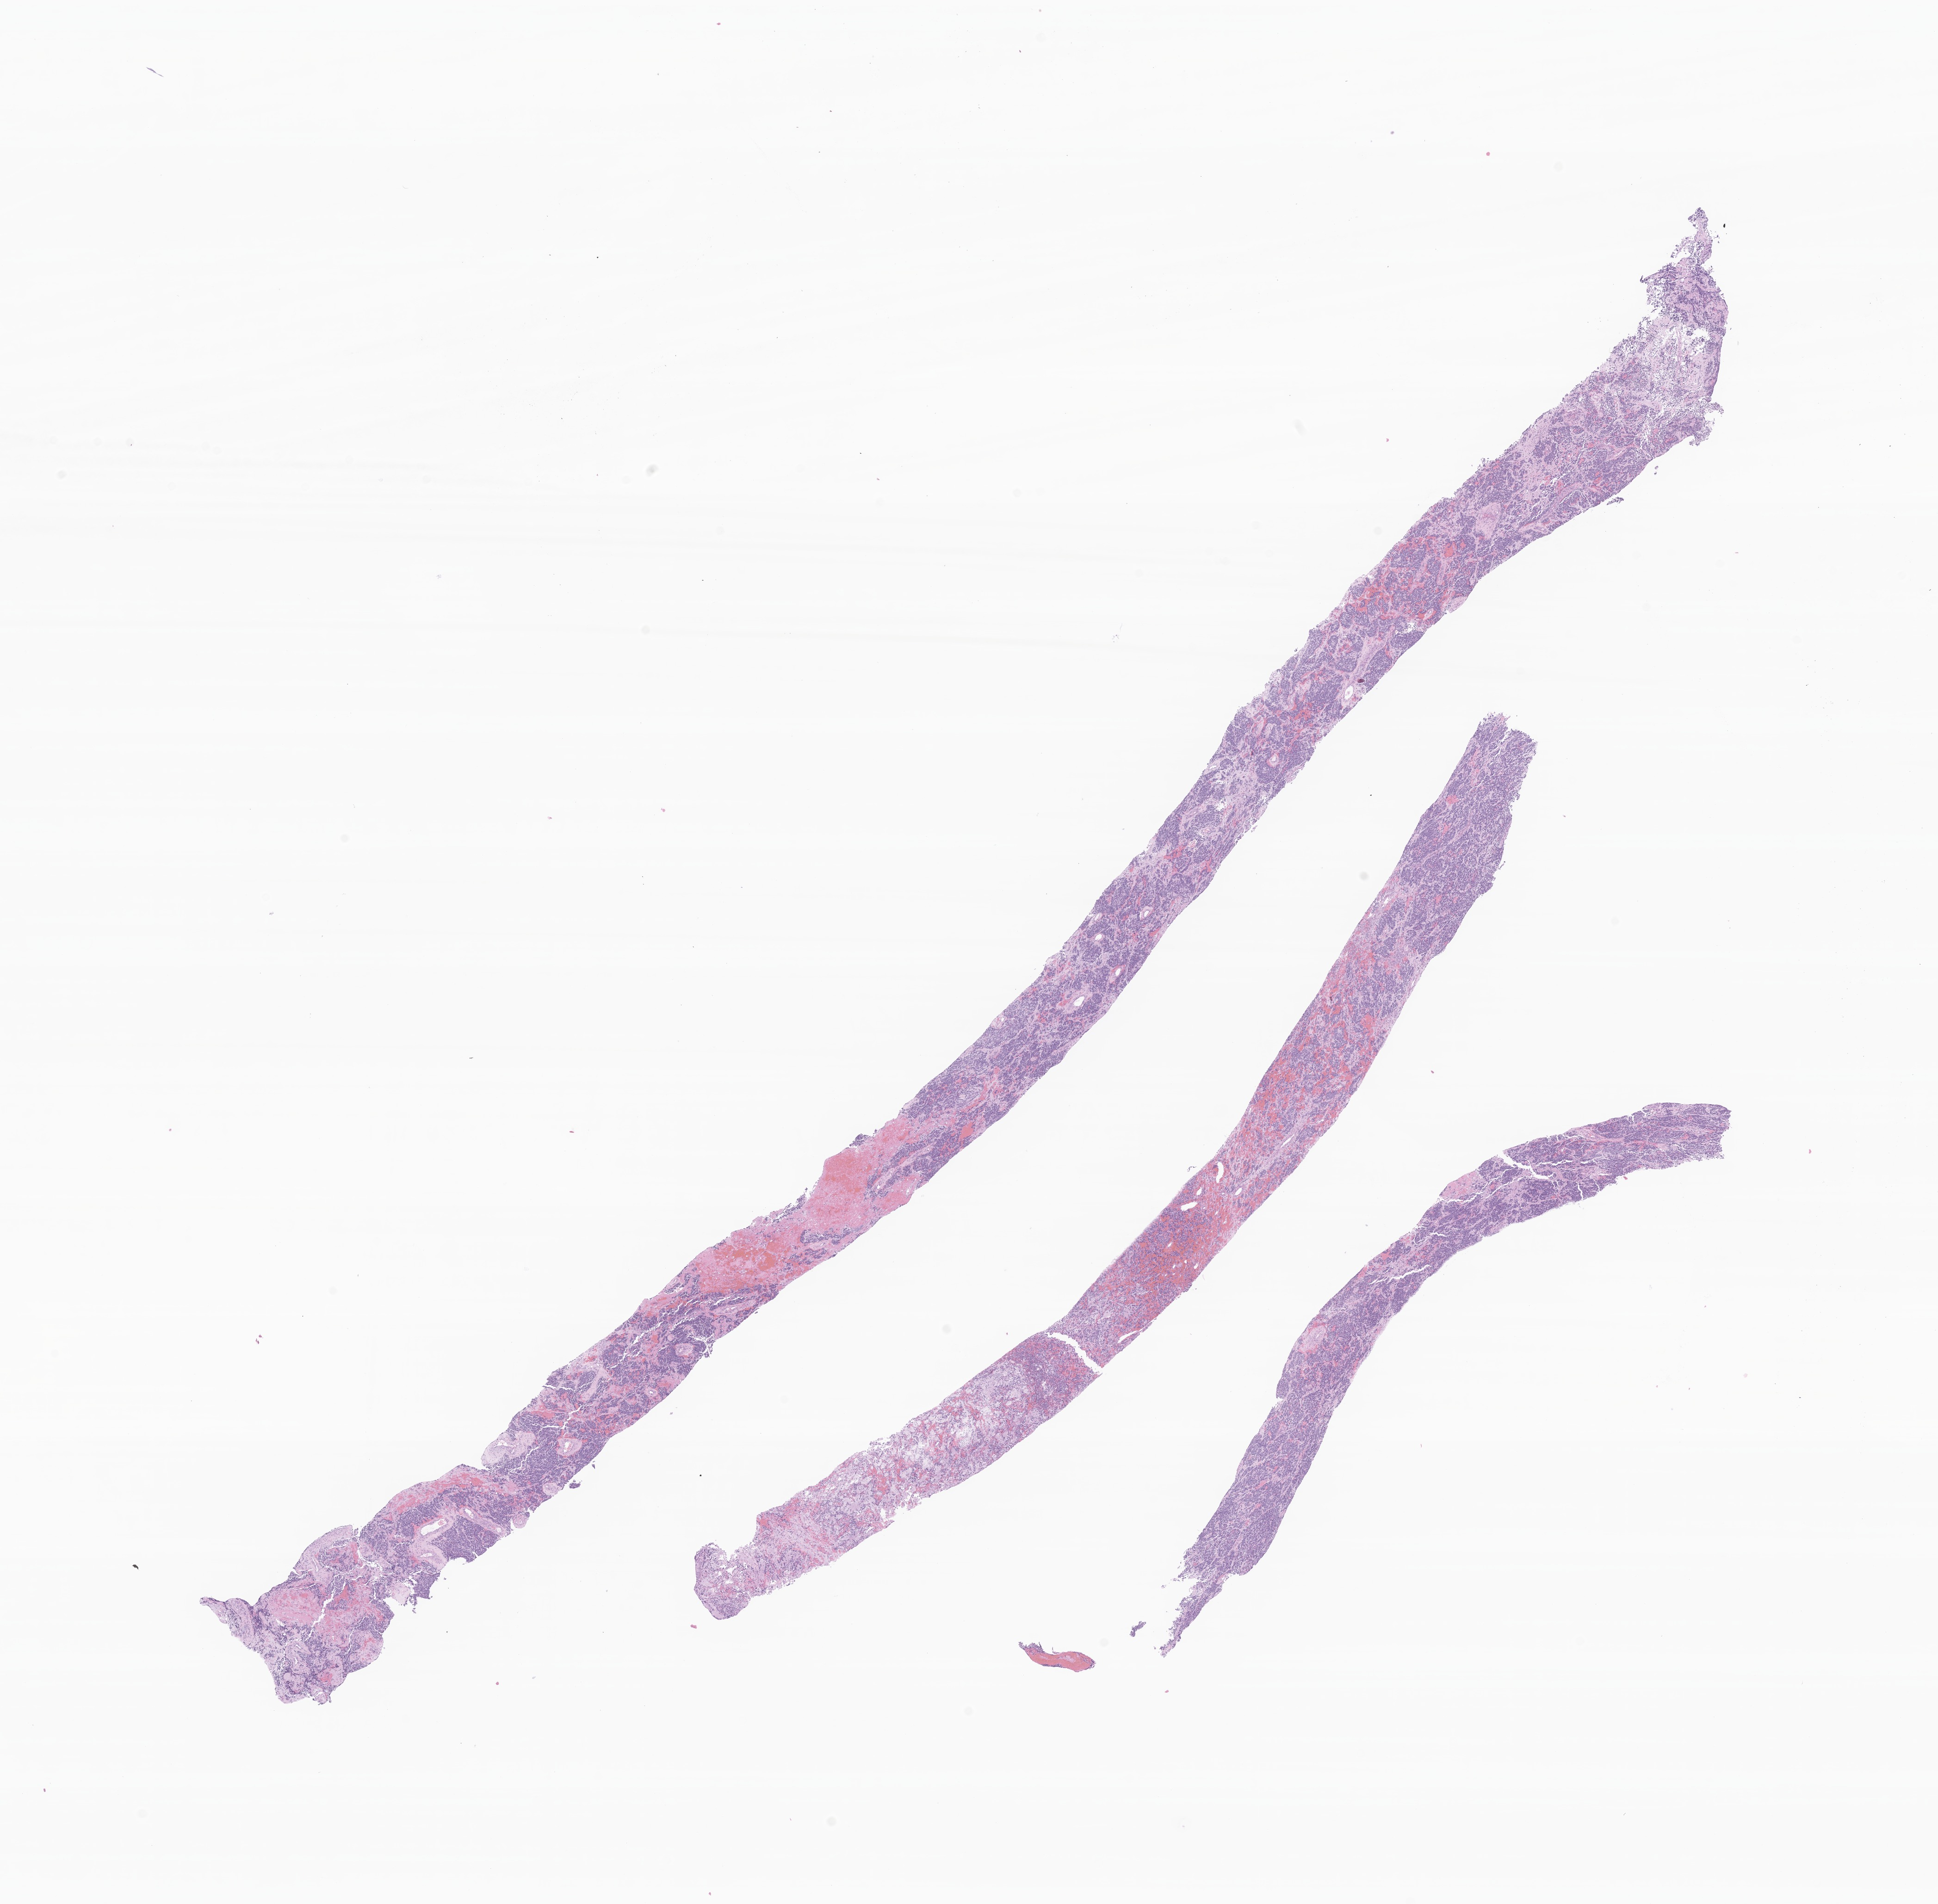
Digitized H&E-stained section of tumor tissue from the abdomen — a low-resolution overview of the entire scanned area, about 17.7 x 17.4 mm. Formalin-fixed paraffin-embedded section. Patient: male, age 66 months (5 years 6 months).
Diagnosis (ICD-O-3 morphology term): Neuroblastoma, NOS.